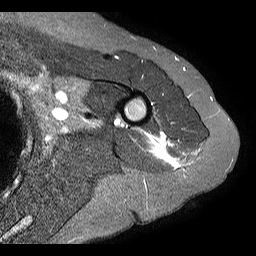
MRI of an extremity soft-tissue mass, one axial slice; slice 3 of 20 in the series (ordered by position); STIR; 4 mm slice thickness; 256 × 256 image matrix, field of view 150 × 150 mm. Female patient. From the clinical record (not read from this slice): histological type: malignant fibrous histiocytoma; grade: low; site of the primary tumour: left arm.
Structures marked on this image (manually delineated by an expert):
- gross tumour volume (mass): bounding box [x1, y1, x2, y2] px = [154, 136, 170, 160]